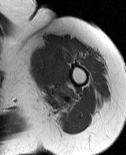
MRI of an extremity soft-tissue mass, one axial slice. Slice 61 of 86 in the series (ordered by position). MR volume resampled by the dataset authors to the PET/CT grid (not the native acquisition matrix). 3.27 mm slice thickness. 126 × 155 image matrix, field of view 123 × 151 mm. Female patient. From the clinical record (not read from this slice): histological type: pleiomorphic leiomyosarcoma; grade: high; site of the primary tumour: left biceps.
Outlined on this slice (expert contour drawn on MRI and transferred to this co-registered scan by the dataset authors):
- gross tumour volume including surrounding oedema: bounding box <29,44,66,98> (left, top, right, bottom; pixels)
- gross tumour volume (mass): <27,47,62,86>